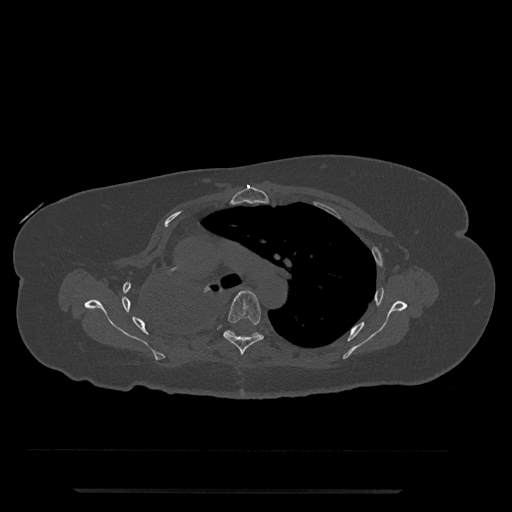
CT including the spine, one axial slice; position 538 of 797 along the scan axis; 120 kVp; bone window (W 1800 / L 400 HU); 512 × 512 image matrix, field of view 440 × 440 mm. Female patient, age 51 years. From the clinical record (not read from this slice): primary cancer: neuro; vertebrae with lytic lesions (as recorded): T8.
Annotated regions visible in this slice (semi-automatically segmented with operator editing):
- T5 vertebra: bounding box <223,290,264,355> (left, top, right, bottom; pixels)
- T6 vertebra: <226,330,259,337>